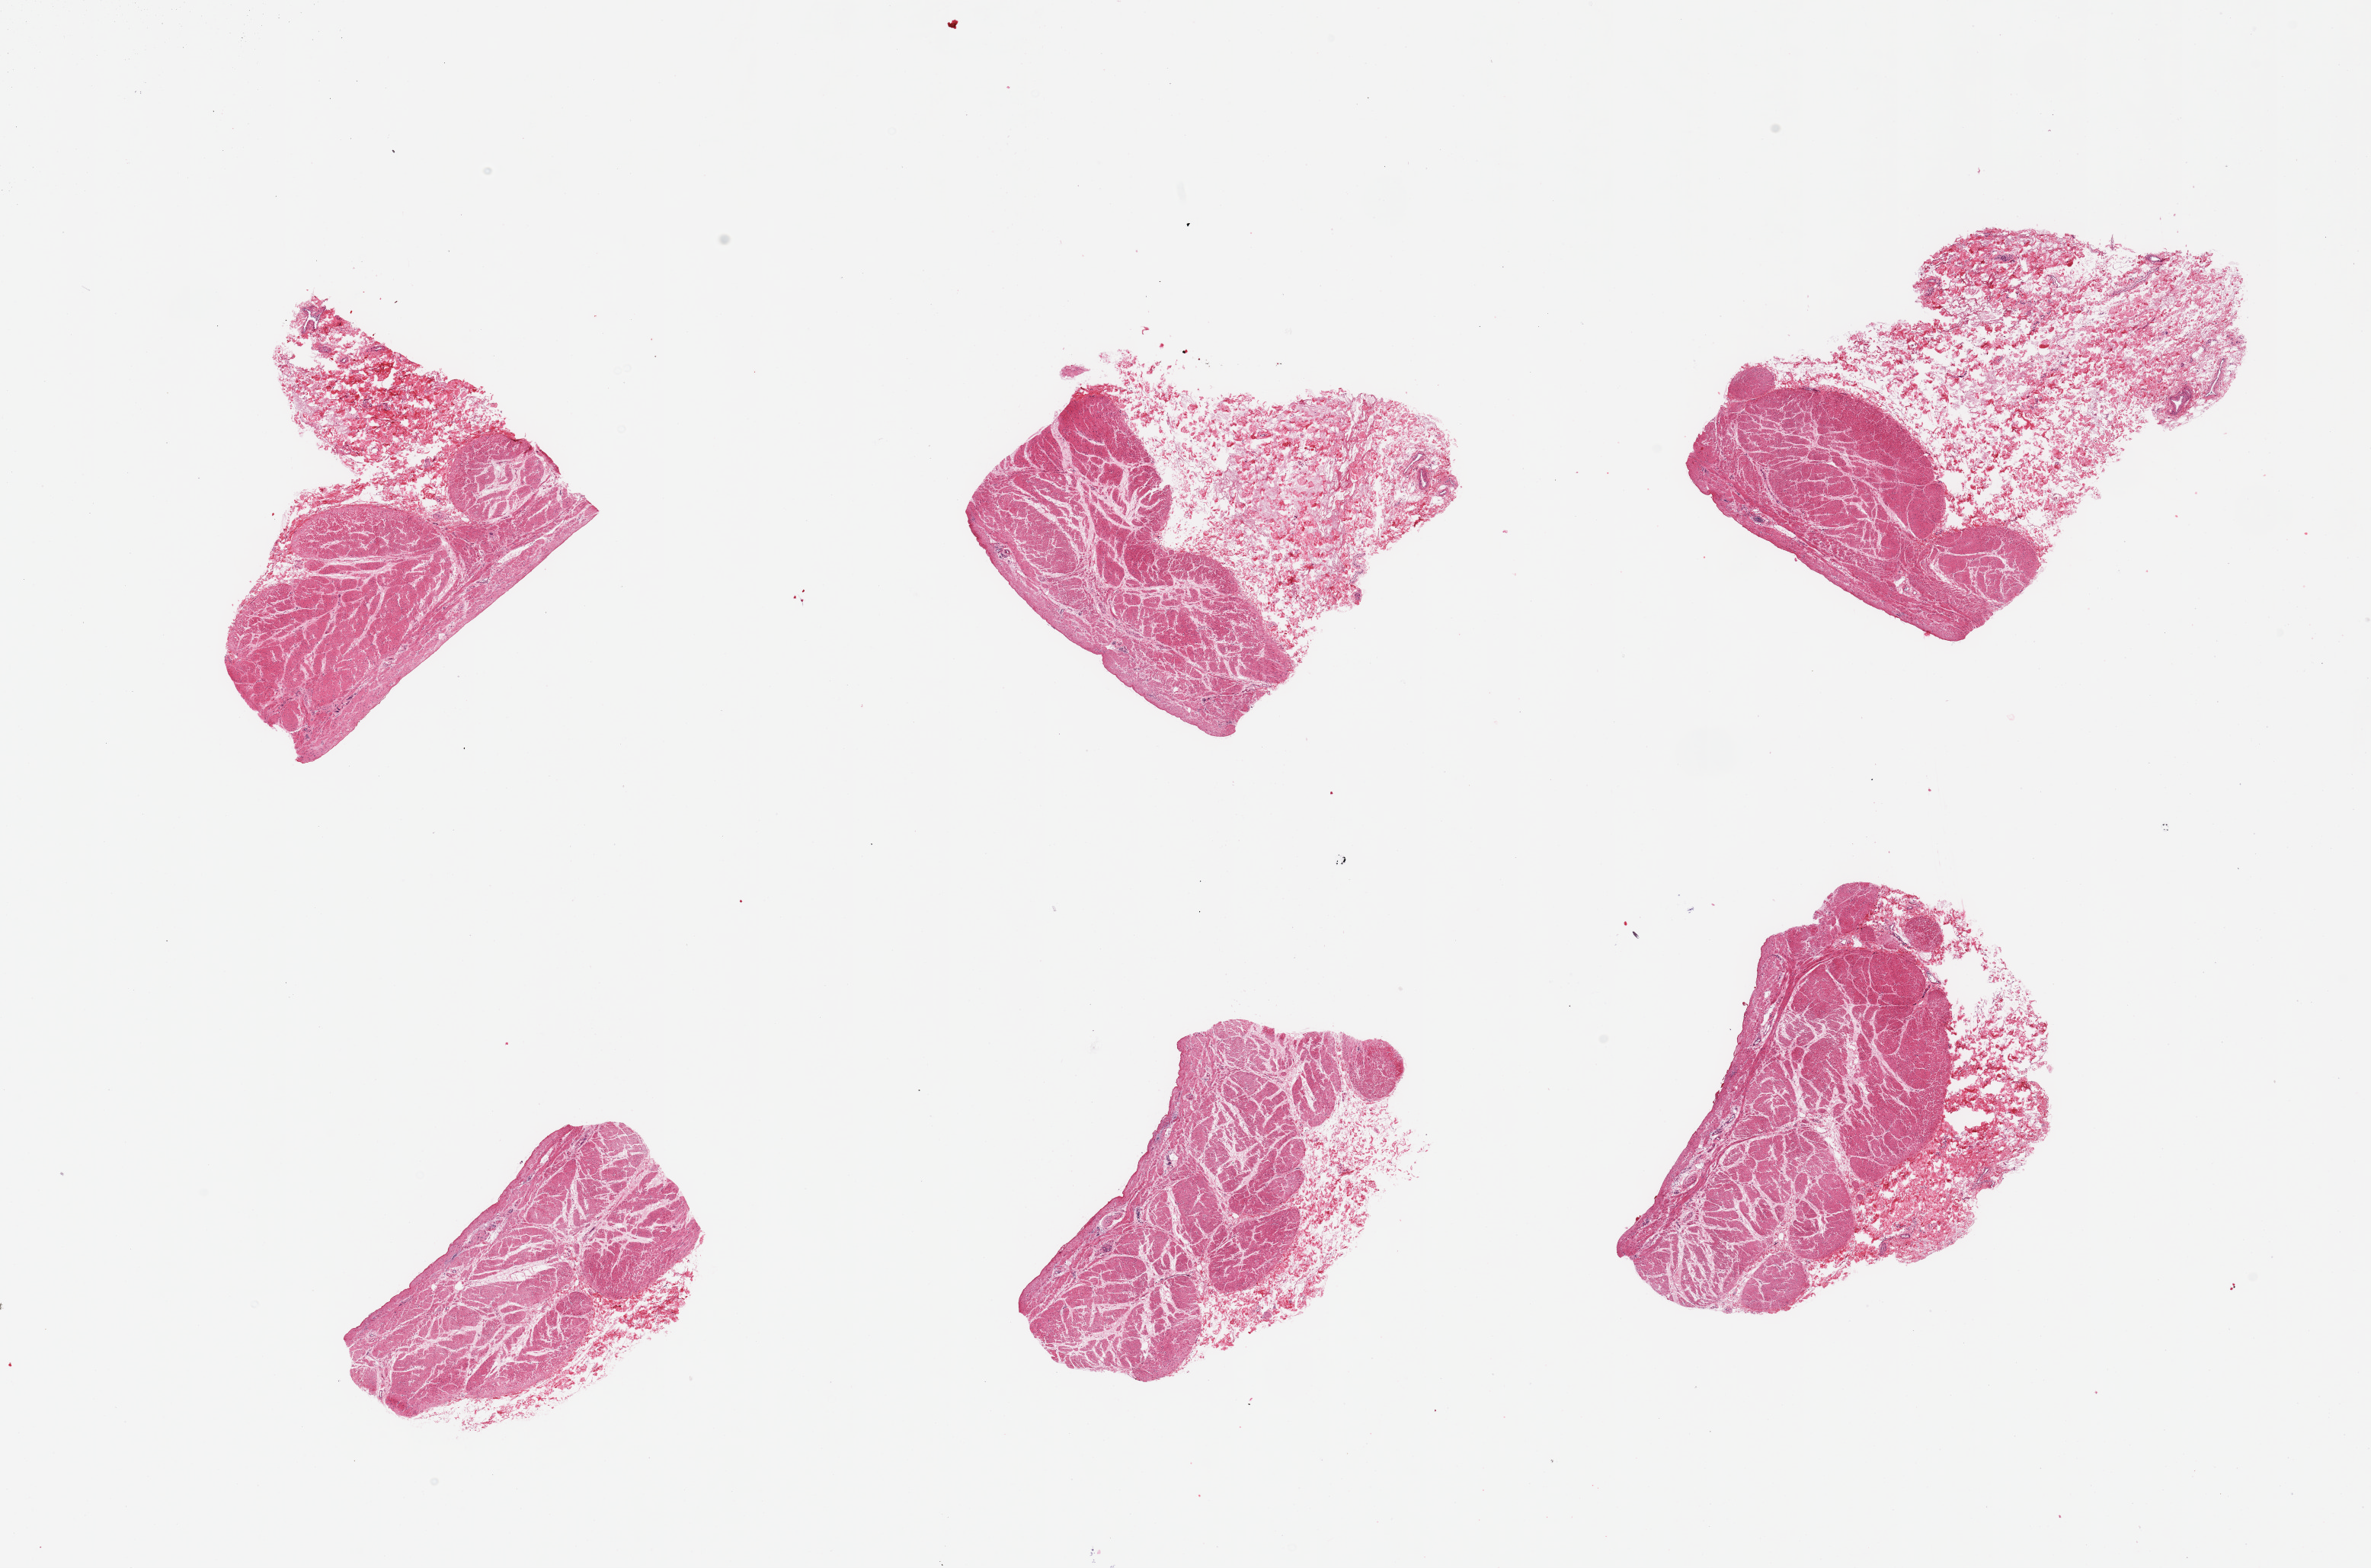
Whole-slide image, hematoxylin and eosin (H&E) stain — low-resolution overview of the scanned area, about 24.6 x 16.3 mm (acquisition: 20x scan), PAXgene-fixed paraffin-embedded (PFPE) section, target tissue: stomach, donor tissue sample. Donor: female.
• pathologist's review note for this sample: 6 pieces, mucosal elements sloughed, all muscularis/serosal fat